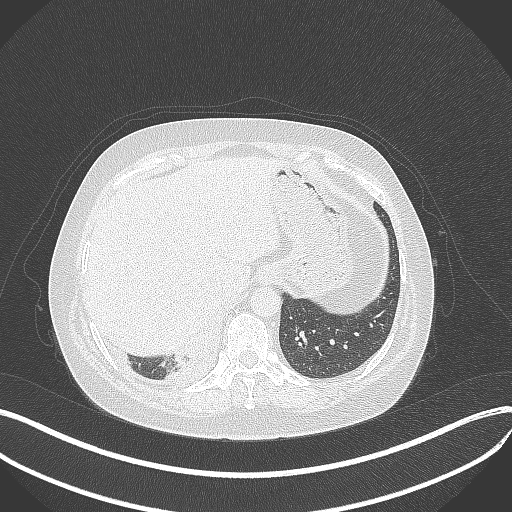
Chest CT, one axial slice; slice 70 of 381 in the series (ordered by position); lung window (W 1500 / L -600 HU); 512 × 512 image matrix, field of view 400 × 400 mm. Female patient, age 56 years. Case-level facts recorded for this patient, not image findings: clinical TNM (as recorded): T2b N1 M0.
Annotated regions visible in this slice (rectangle marked by the reading radiologist):
- lung tumour (recorded histology: small cell carcinoma): bounding box (x1, y1, x2, y2) in pixels: (172, 345, 196, 371)